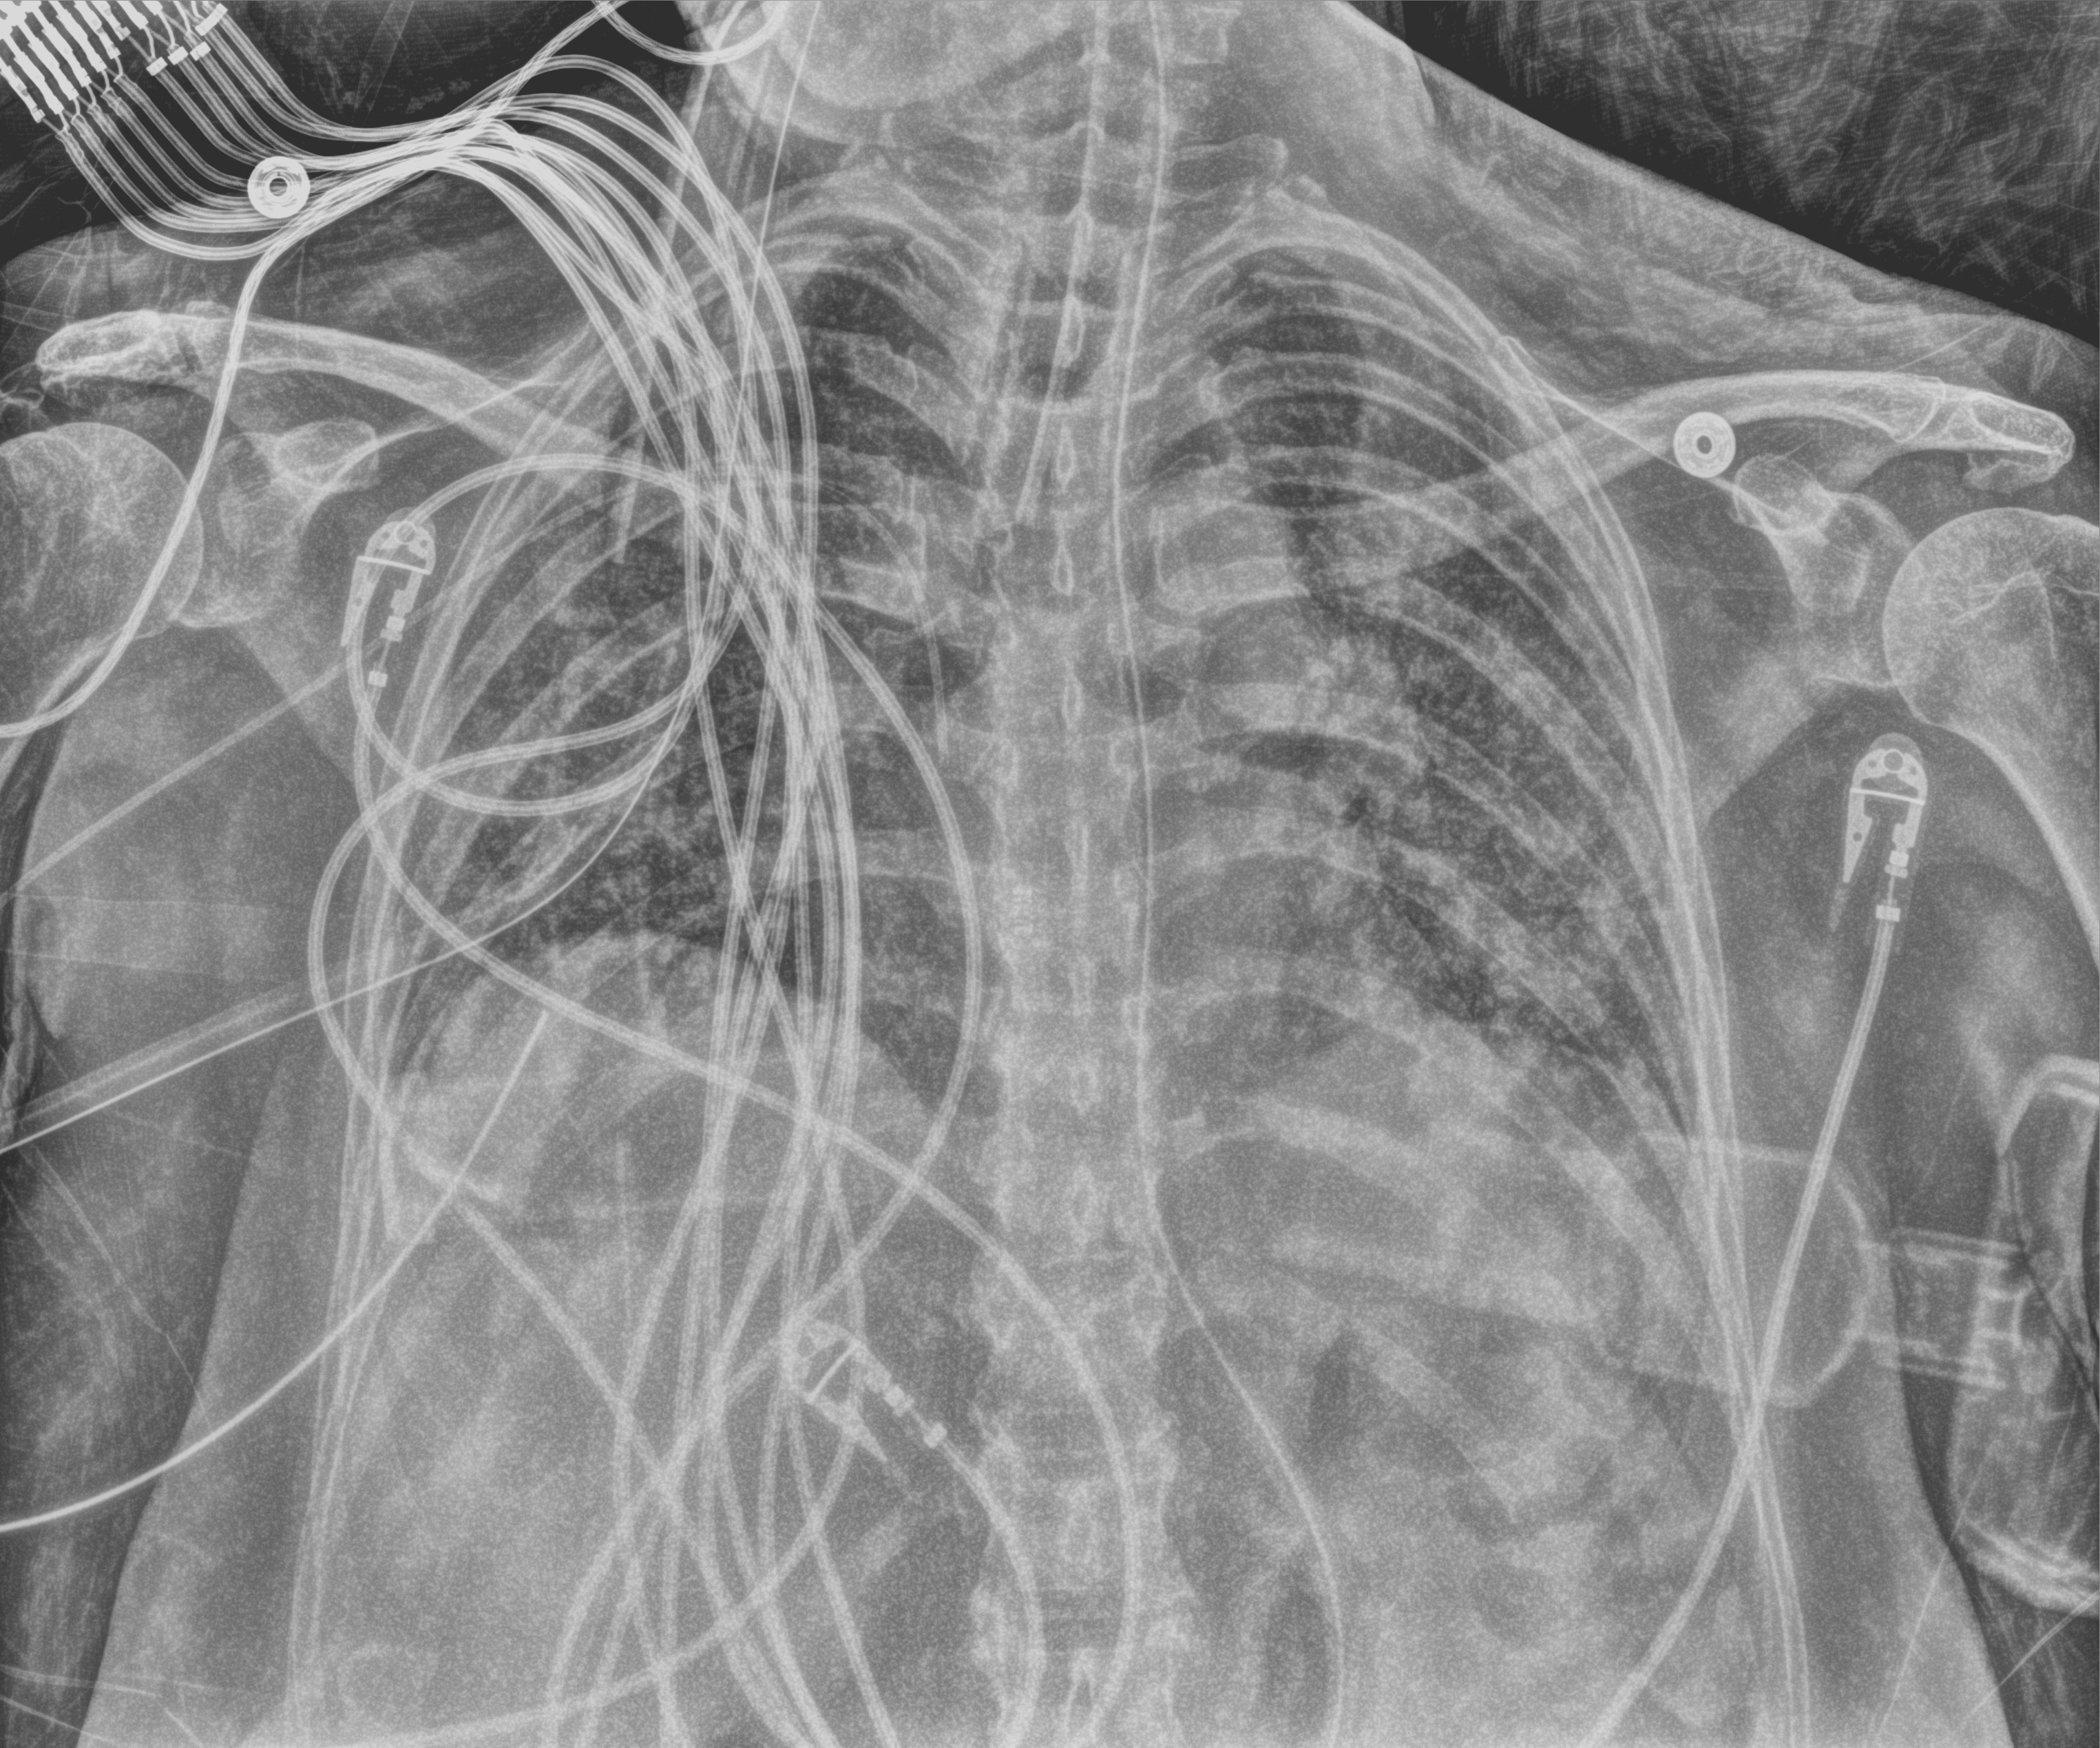
Portable chest radiograph; anteroposterior (AP) projection. Patient hospitalised with COVID-19; female, aged 60–74 years.
Hospital-stay facts (about this admission, not read from this image; timing relative to this image not recorded):
- admitted to intensive care during this hospital stay: yes